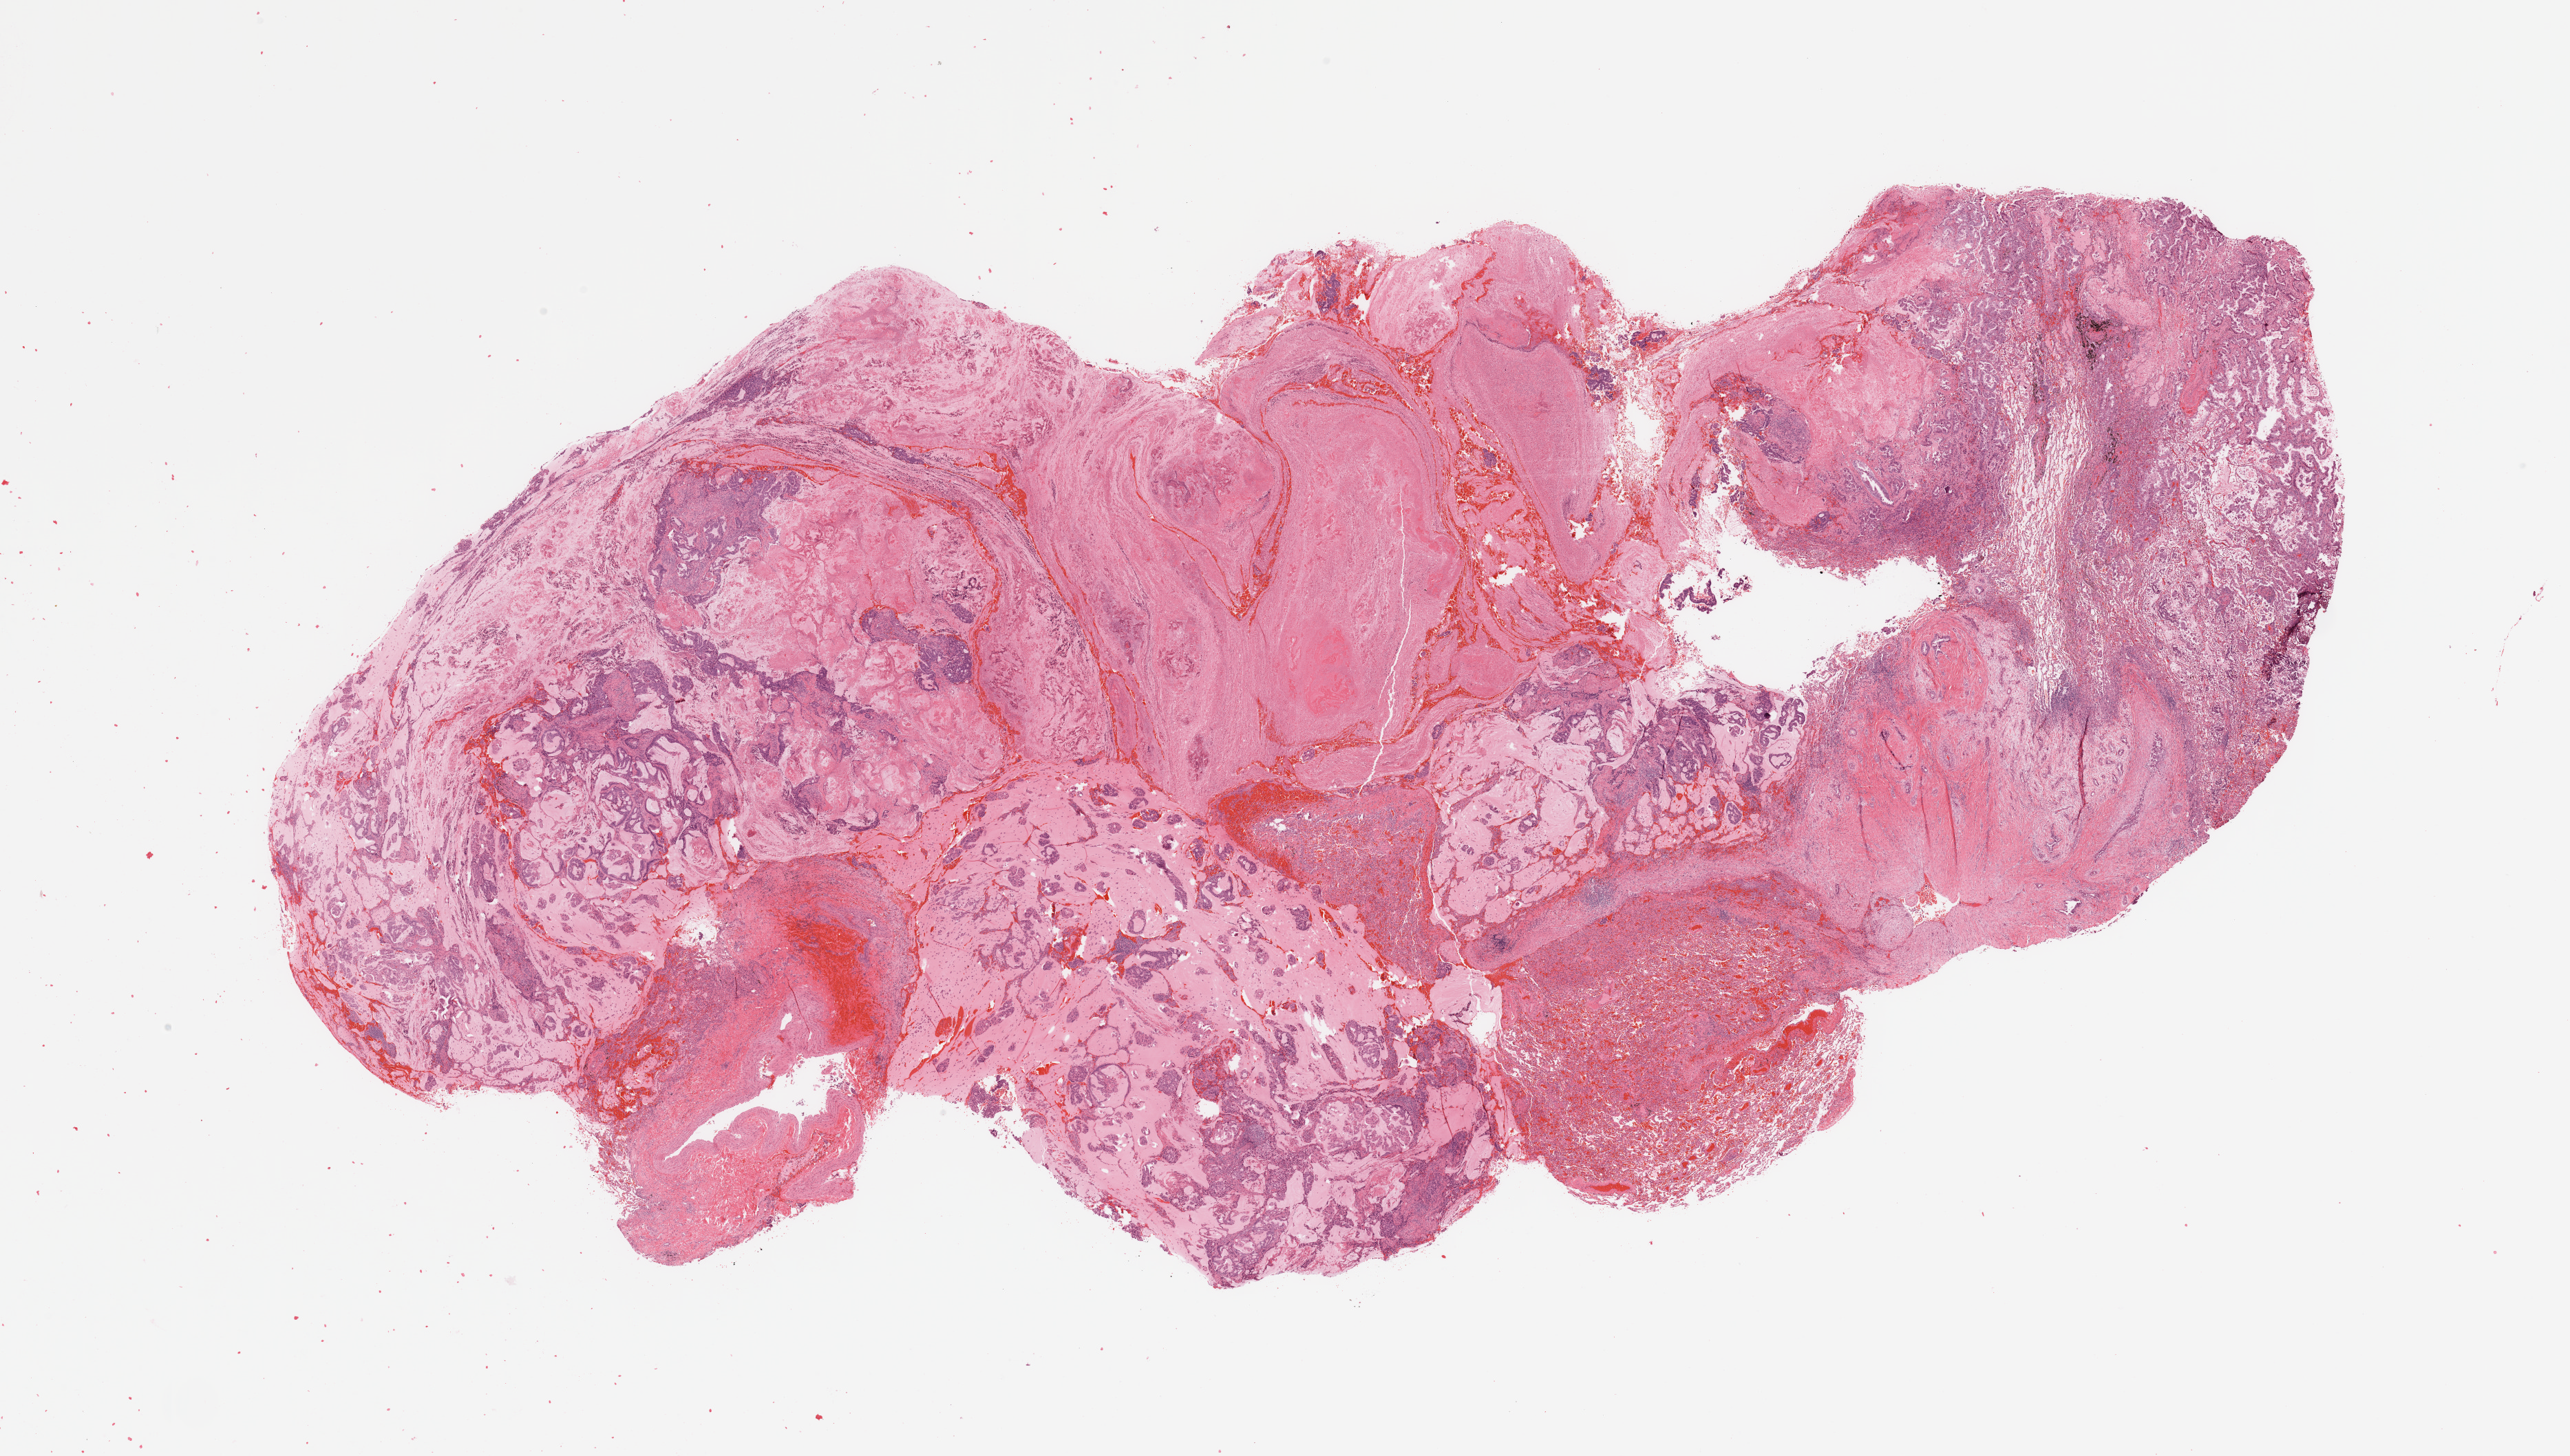
Hematoxylin and eosin (H&E) stained whole-slide image — shown as a low-resolution overview of the whole scanned area (about 29.5 x 16.7 mm, slide scanned at 20x); tumour tissue sample, lung. Patient: male, age 40 years. Histologic grade: G2 (moderately differentiated).
* AJCC pathologic stage: IB
* primary tumour site (as recorded): right lower lobe
* diagnosis: Adenocarcinoma, NOS